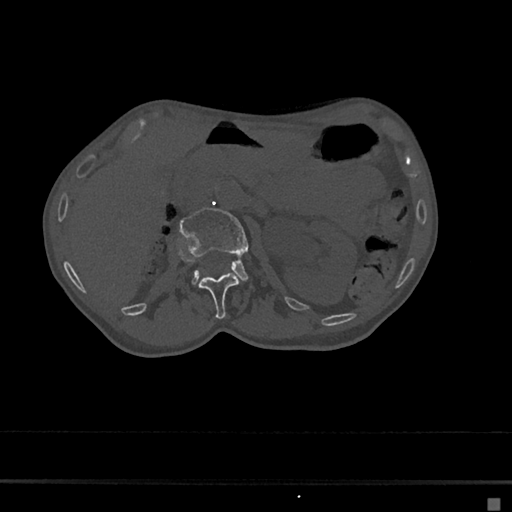
CT including the spine, one axial slice. Slice 48 of 797 in the series (ordered by position). Reconstruction kernel Br40s/3. Bone window (W 1800 / L 400 HU). 0.5 mm slice thickness. 512 × 512 image matrix, field of view 360 × 360 mm. Female patient, age 68 years. Case-level facts recorded for this patient, not image findings: primary cancer: renal.
Structures marked on this image (semi-automatically segmented with operator editing):
- L1 vertebra: bounding box (x1, y1, x2, y2) in pixels: (199, 273, 238, 320)
- L2 vertebra: (180, 208, 249, 283)